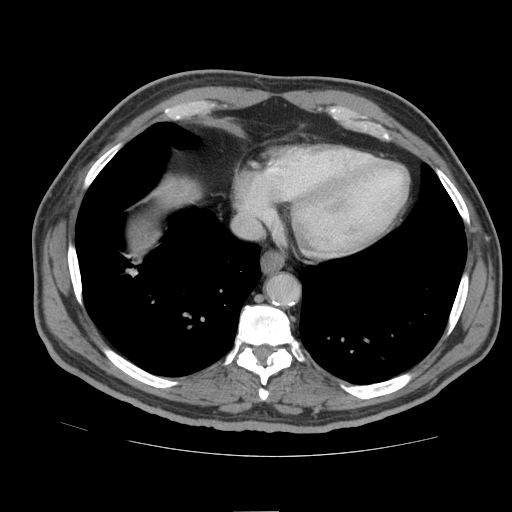
Contrast-enhanced abdominal CT (liver protocol), one axial slice. Slice 82 of 105 in the series (ordered by position). Reconstruction kernel STANDARD. 140 kVp. Soft-tissue window (W 400 / L 40 HU). 2.5 mm slice thickness. 512 × 512 image matrix, field of view 380 × 380 mm. From the clinical record (not read from this slice): diagnosis: hepatocellular carcinoma (patient treated with transarterial chemoembolisation; whether this scan precedes or follows treatment is not stated here); TNM stage (as recorded): Stage-IIIB; Child-Pugh class: A; tumour nodularity: multinodular.
Outlined on this slice (semi-automatically segmented with operator editing):
- liver parenchyma outside the tumour (the mass and vessels are separate outlines, so this box may not span the whole liver): box from (x=158, y=182) to (x=188, y=200) px